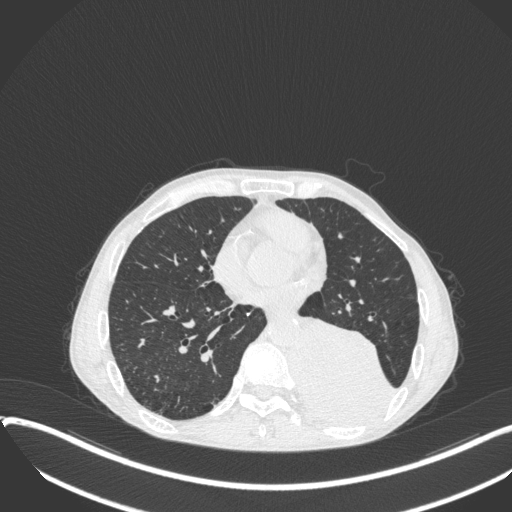
Chest CT, one axial slice. Position 143 of 400 along the scan axis. Lung window (W 1500 / L -600 HU). 1 mm slice thickness. 512 × 512 image matrix, field of view 400 × 400 mm. Male patient, age 57 years. Case-level facts recorded for this patient, not image findings: clinical TNM (as recorded): T4 N0 M0.
Outlined on this slice (bounding box drawn by a radiologist):
- lung tumour (recorded histology: squamous cell carcinoma): bounding box [x1, y1, x2, y2] px = [290, 317, 392, 433]